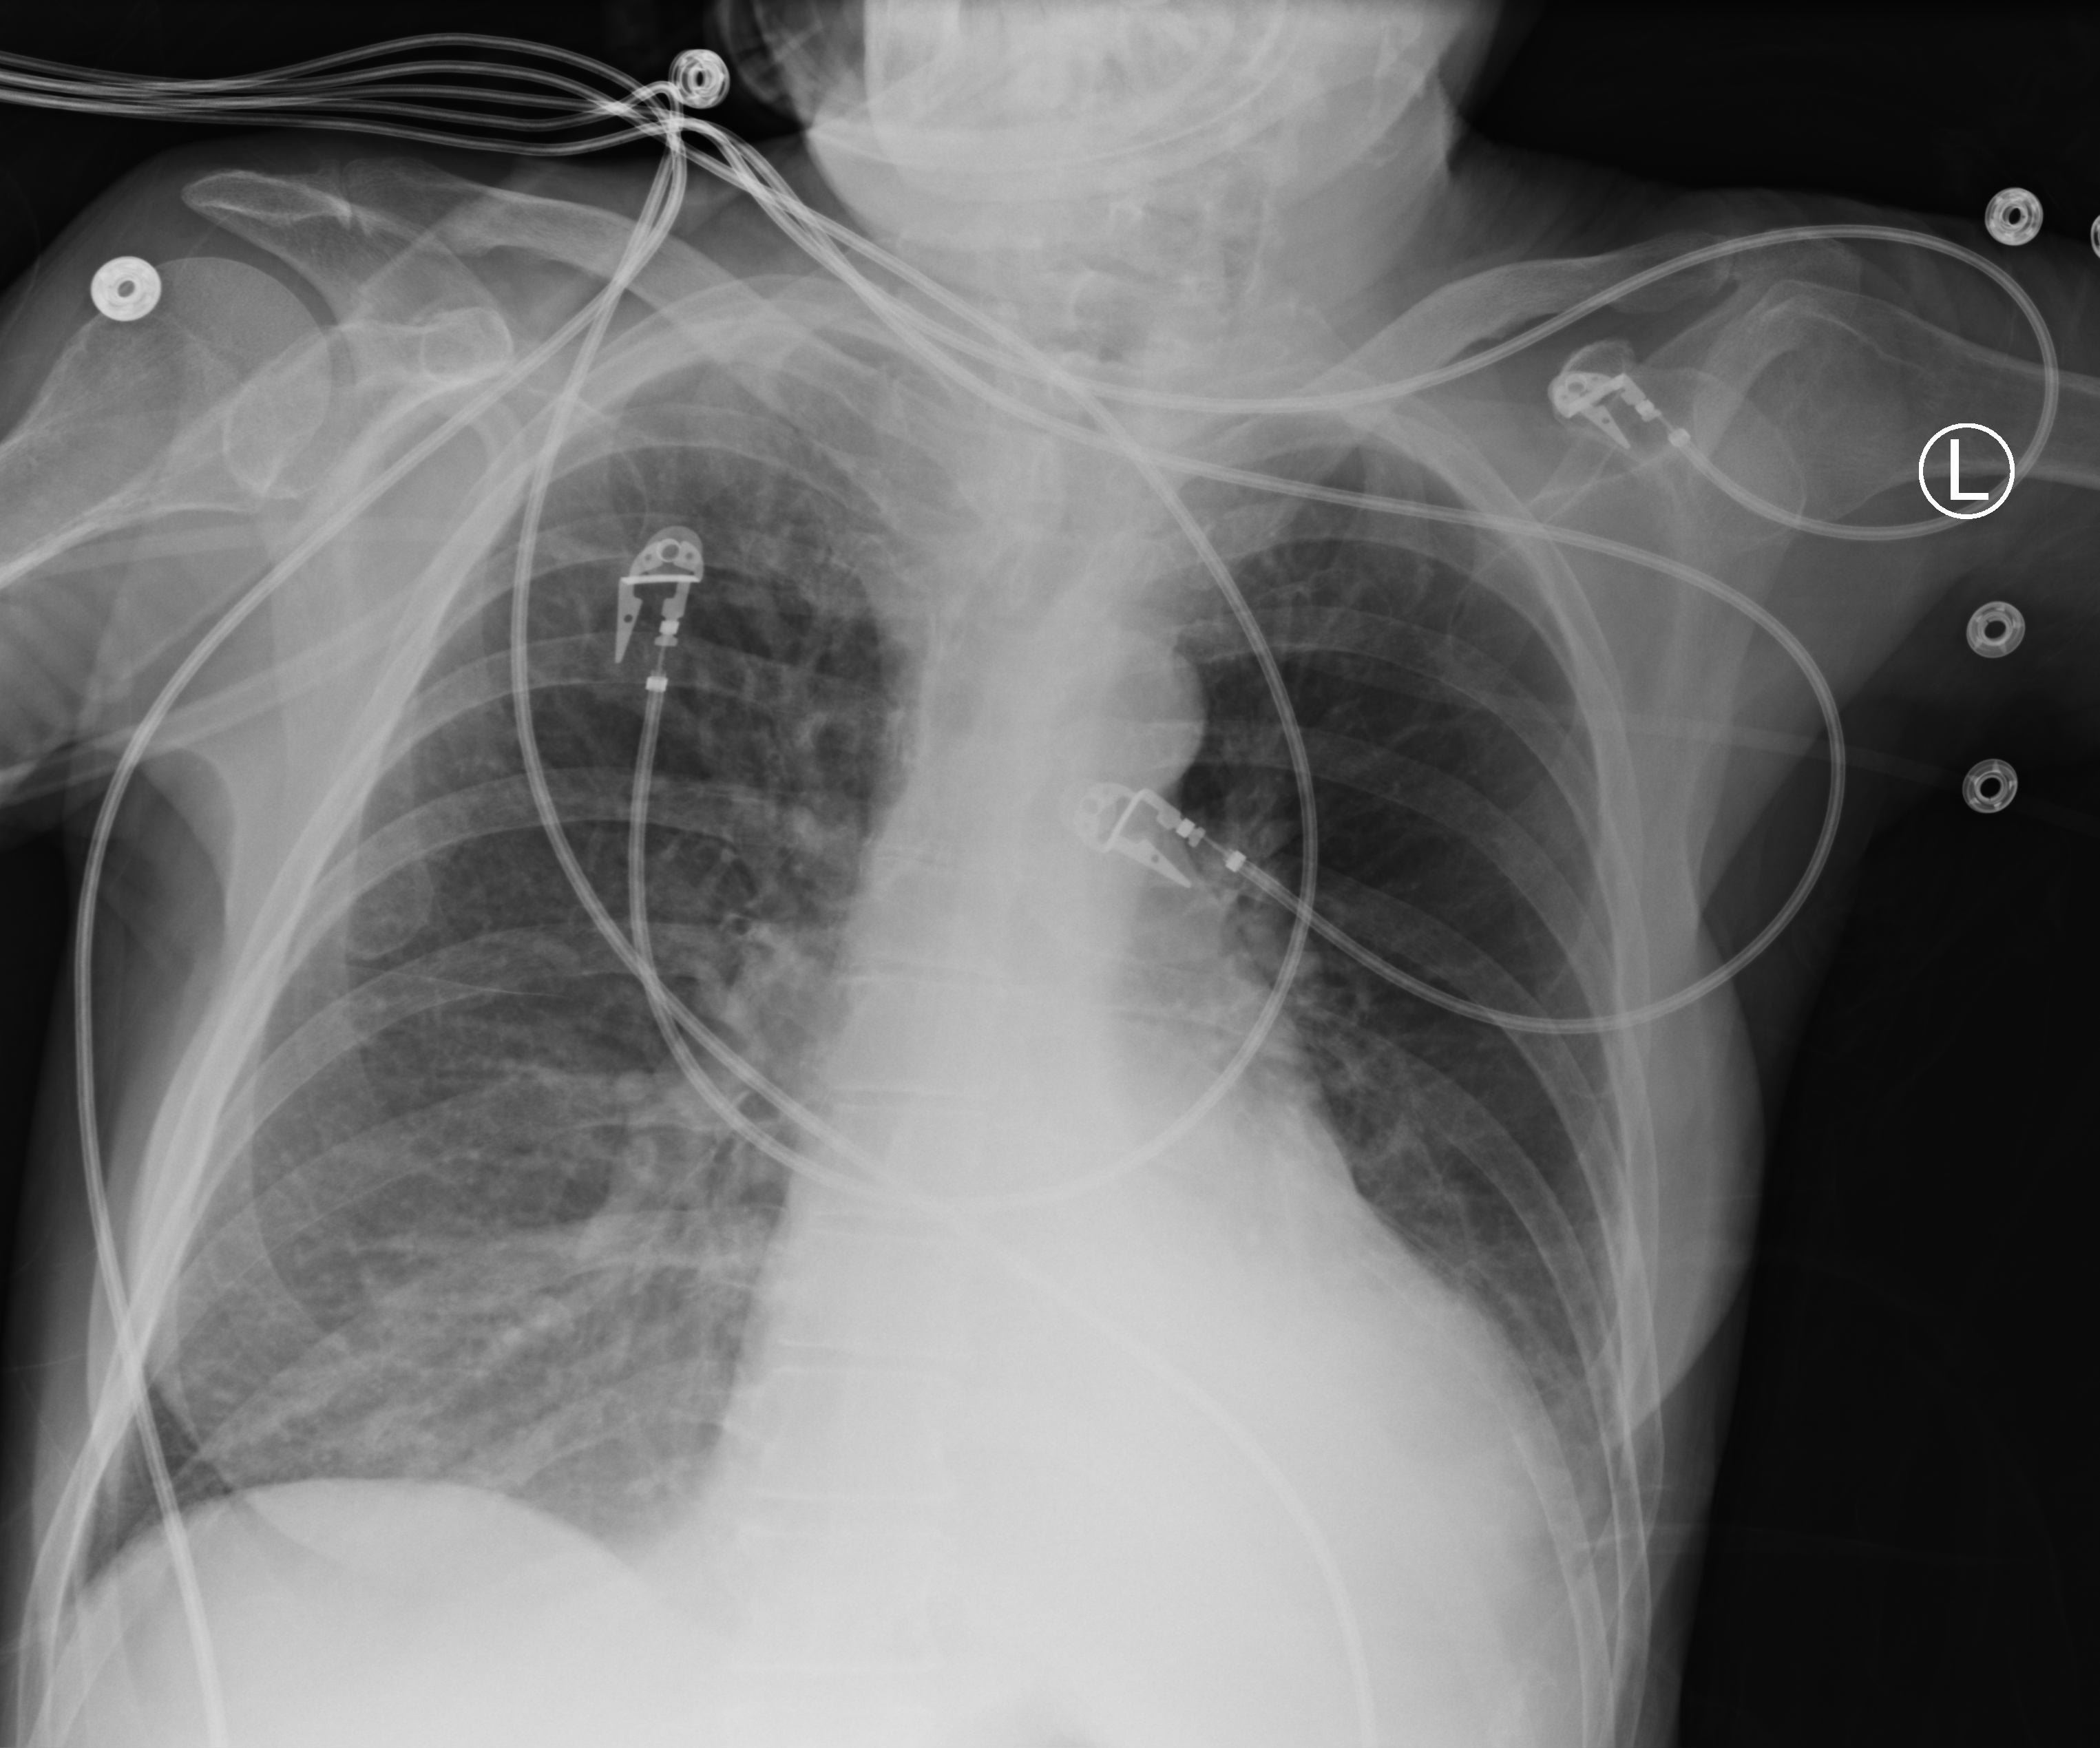
Bedside chest radiograph (computed radiography), anteroposterior (AP) projection. Female patient hospitalised with COVID-19, age 60–74 years.
Admission-level facts for this patient (not findings on this image; timing relative to this image not recorded): mechanically ventilated during this hospital stay: yes; admitted to intensive care during this hospital stay: yes.